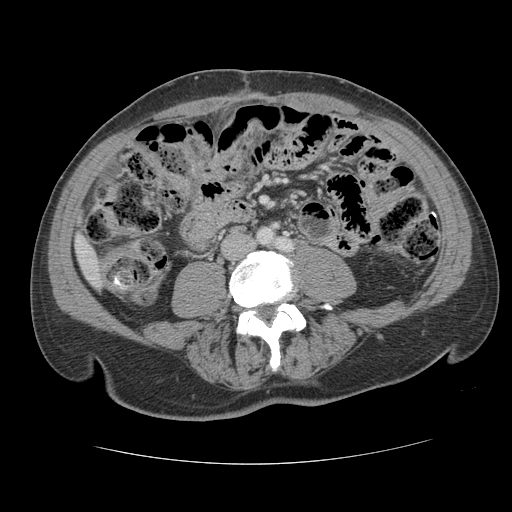
Contrast-enhanced abdominal CT, one axial slice; slice 19 of 134 in the series (ordered by position); reconstruction kernel STANDARD; intravenous contrast given; soft-tissue window (W 400 / L 40 HU); 2.5 mm slice thickness; 512 × 512 image matrix. Male patient, age 68 years. Case-level facts recorded for this patient, not image findings: diagnosis: colorectal cancer liver metastases, imaged before liver resection; multiple liver metastases: yes; largest metastasis: 2.2 cm; chemotherapy before resection: no.
Structures marked on this image (outlined manually by an expert reader):
- liver: box from (x=77, y=239) to (x=98, y=284) px
- planned liver remnant (the part of the liver to remain after resection): (x=77, y=239)–(x=98, y=283)